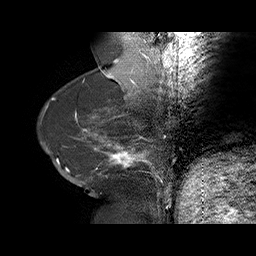
Breast MRI (dynamic contrast-enhanced), one sagittal slice. Position 23 of 75 along the scan axis. Dynamic contrast-enhanced series, time point 2 of 6 at this slice position (early post-contrast). 1.5 T. TE 4.5 ms, TR 32.4 ms. 3 mm slice thickness. 256 × 256 image matrix, field of view 180 × 180 mm. Female patient. From the clinical record (not read from this slice): setting: breast cancer imaged before/during neoadjuvant chemotherapy; receptor status: HR-positive, HER2-negative.
Structures marked on this image (semi-automatic segmentation, software-assisted and operator-edited):
- analysis volume of interest (the breast-tissue region the enhancement analysis was run in; not a lesion): bounding box (x1, y1, x2, y2) in pixels: (58, 134, 166, 191)
- tumour enhancement mask (voxels above the 100 % enhancement threshold inside the analysis volume of interest): (66, 144, 151, 171)